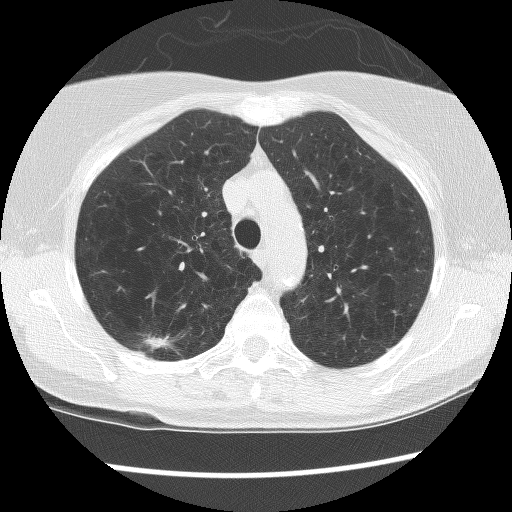
Low-dose screening chest CT, axial slice. Second annual screen. Lung window (W 1500 / L -600 HU). Lung (sharp) reconstruction kernel (BONE). Slice 32 of 134 in the series. Female, age 63 years at enrolment. Former smoker at enrolment.
Lesion marked by an expert reader, box from (x=131, y=319) to (x=194, y=368) px. The exam's reader record, not a measurement of the box and not confirmed to be the same lesion: non-calcified nodule or mass ≥4 mm, right upper lobe, 16 × 7 mm, spiculated (stellate) margins, mixed attenuation, pre-existing on the prior screen: yes; interval growth: yes.